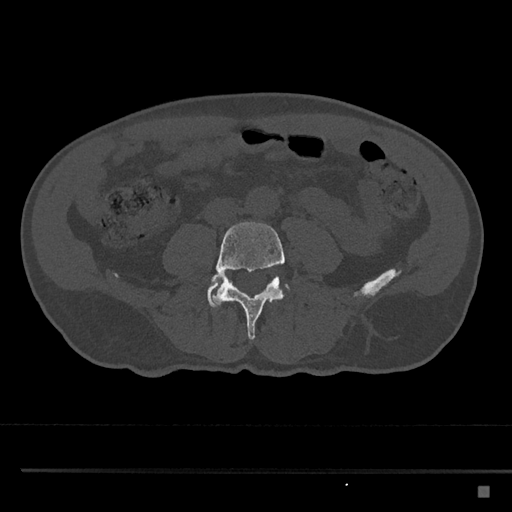
CT including the spine, one axial slice; position 631 of 797 along the scan axis; reconstruction kernel Br40s/3; 120 kVp; bone window (W 1800 / L 400 HU); 0.5 mm slice thickness; 512 × 512 image matrix, field of view 391 × 391 mm. Male patient, age 59 years. From the clinical record (not read from this slice): primary cancer: prostate.
Annotated regions visible in this slice (semi-automatic segmentation, software-assisted and operator-edited):
- L4 vertebra: bounding box <213,221,288,340> (left, top, right, bottom; pixels)
- L5 vertebra: <207,275,289,308>